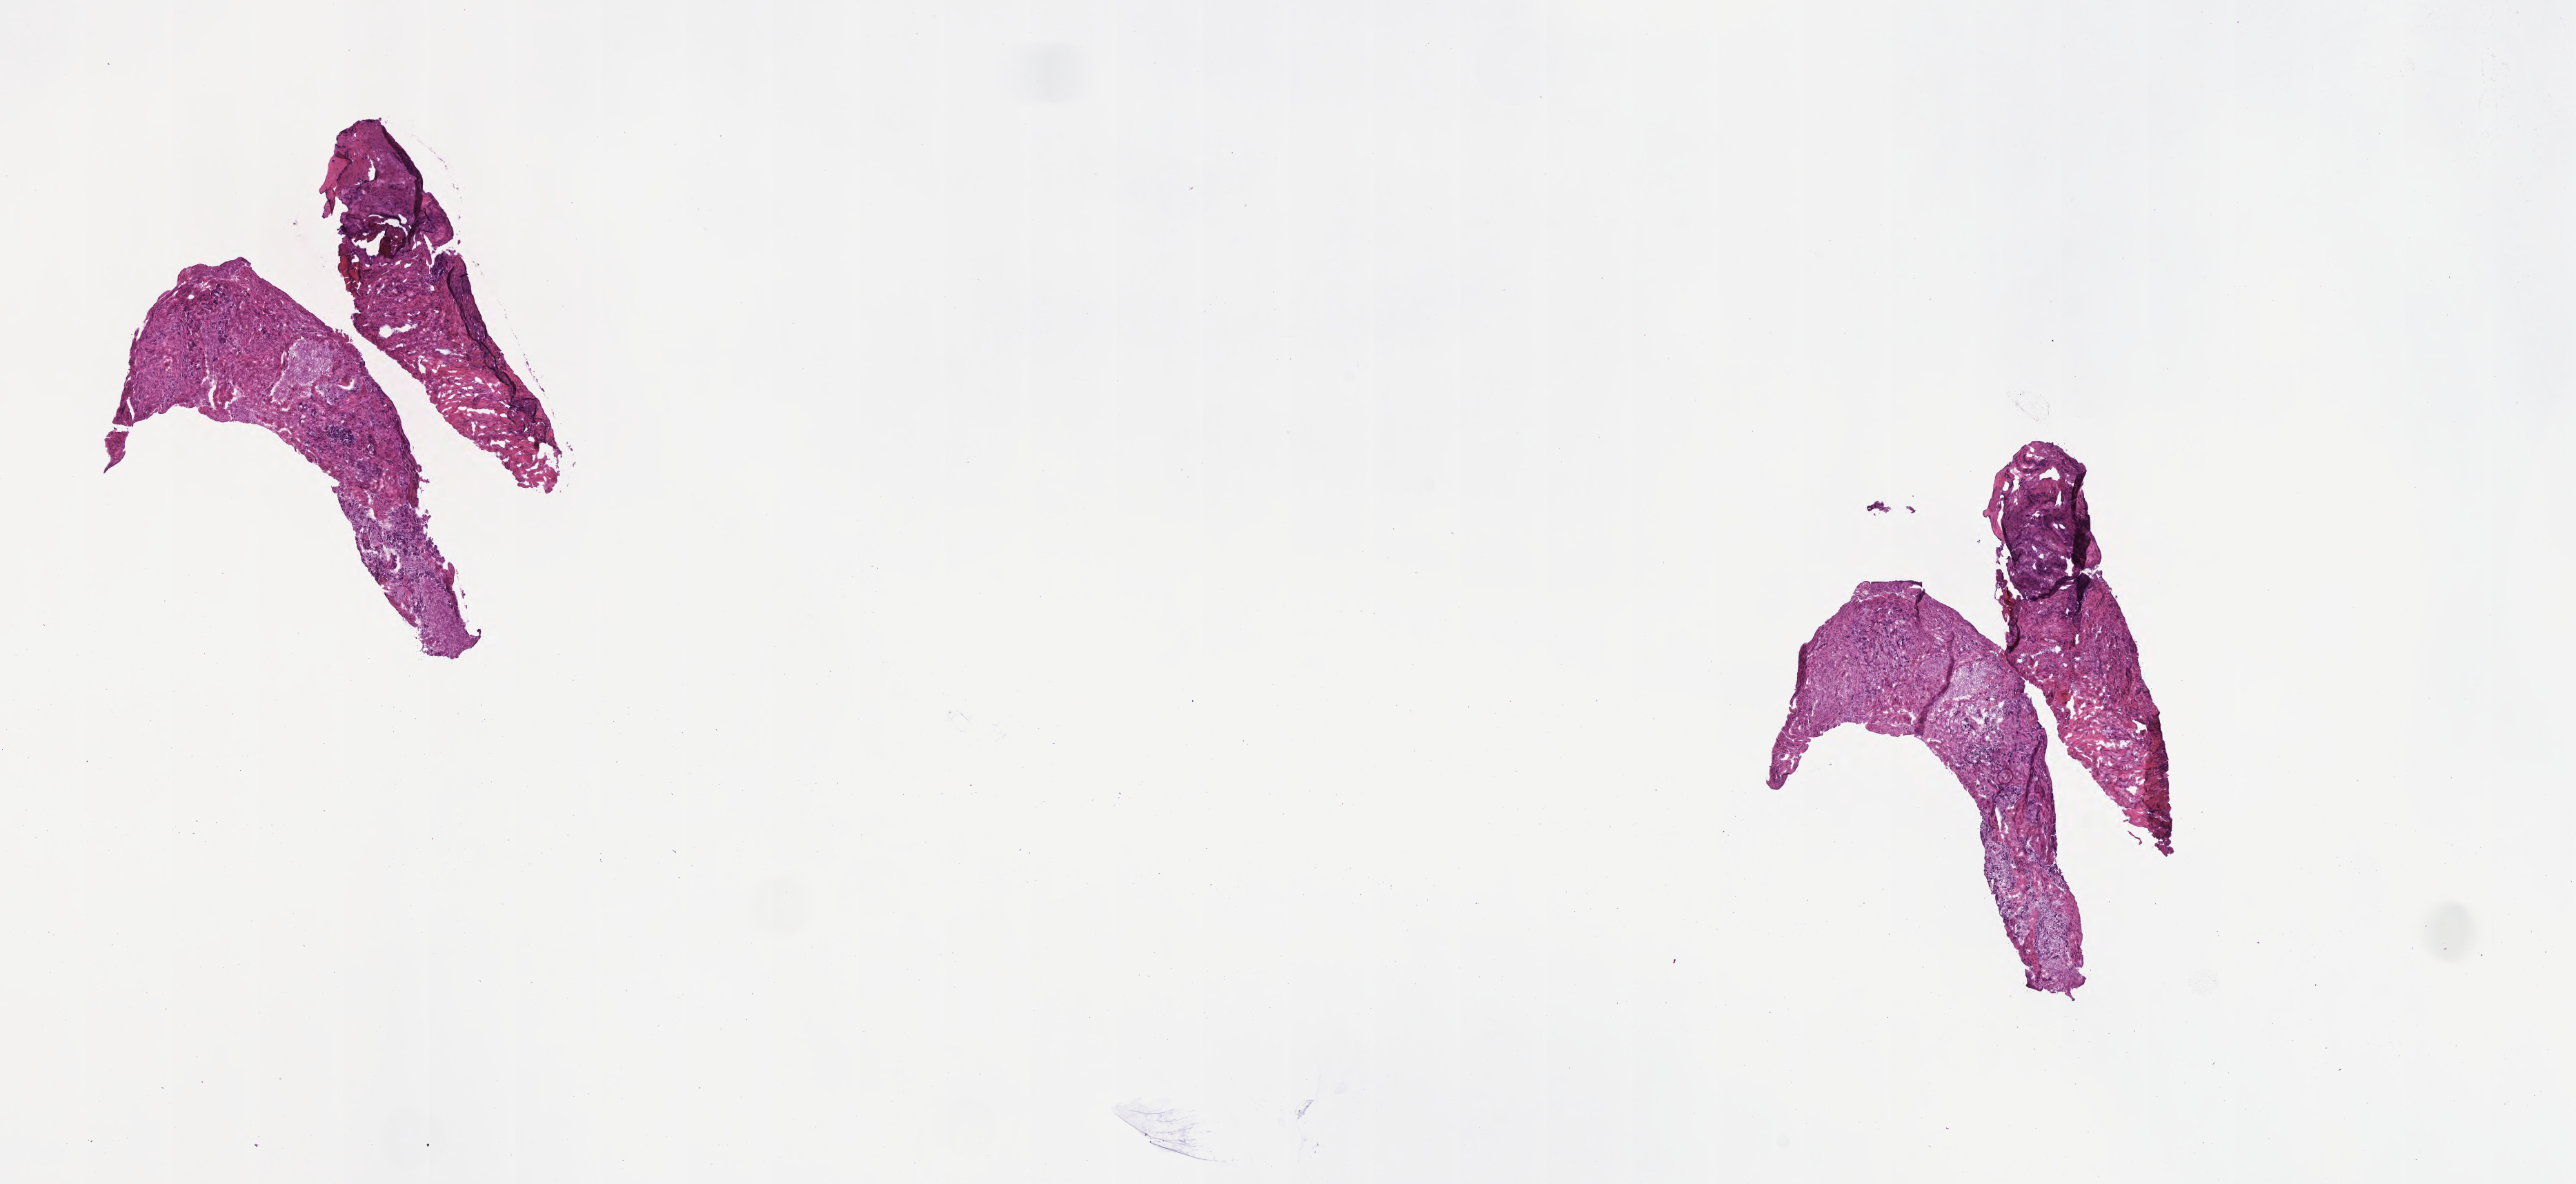
Digitized H&E-stained section of tumor tissue from the posterior mediastinum — low-resolution overview of the scanned area, about 15.1 x 6.9 mm; frozen section. Patient male; age 61 months (5 years 1 month).
Recorded diagnosis: Neuroblastoma, NOS.